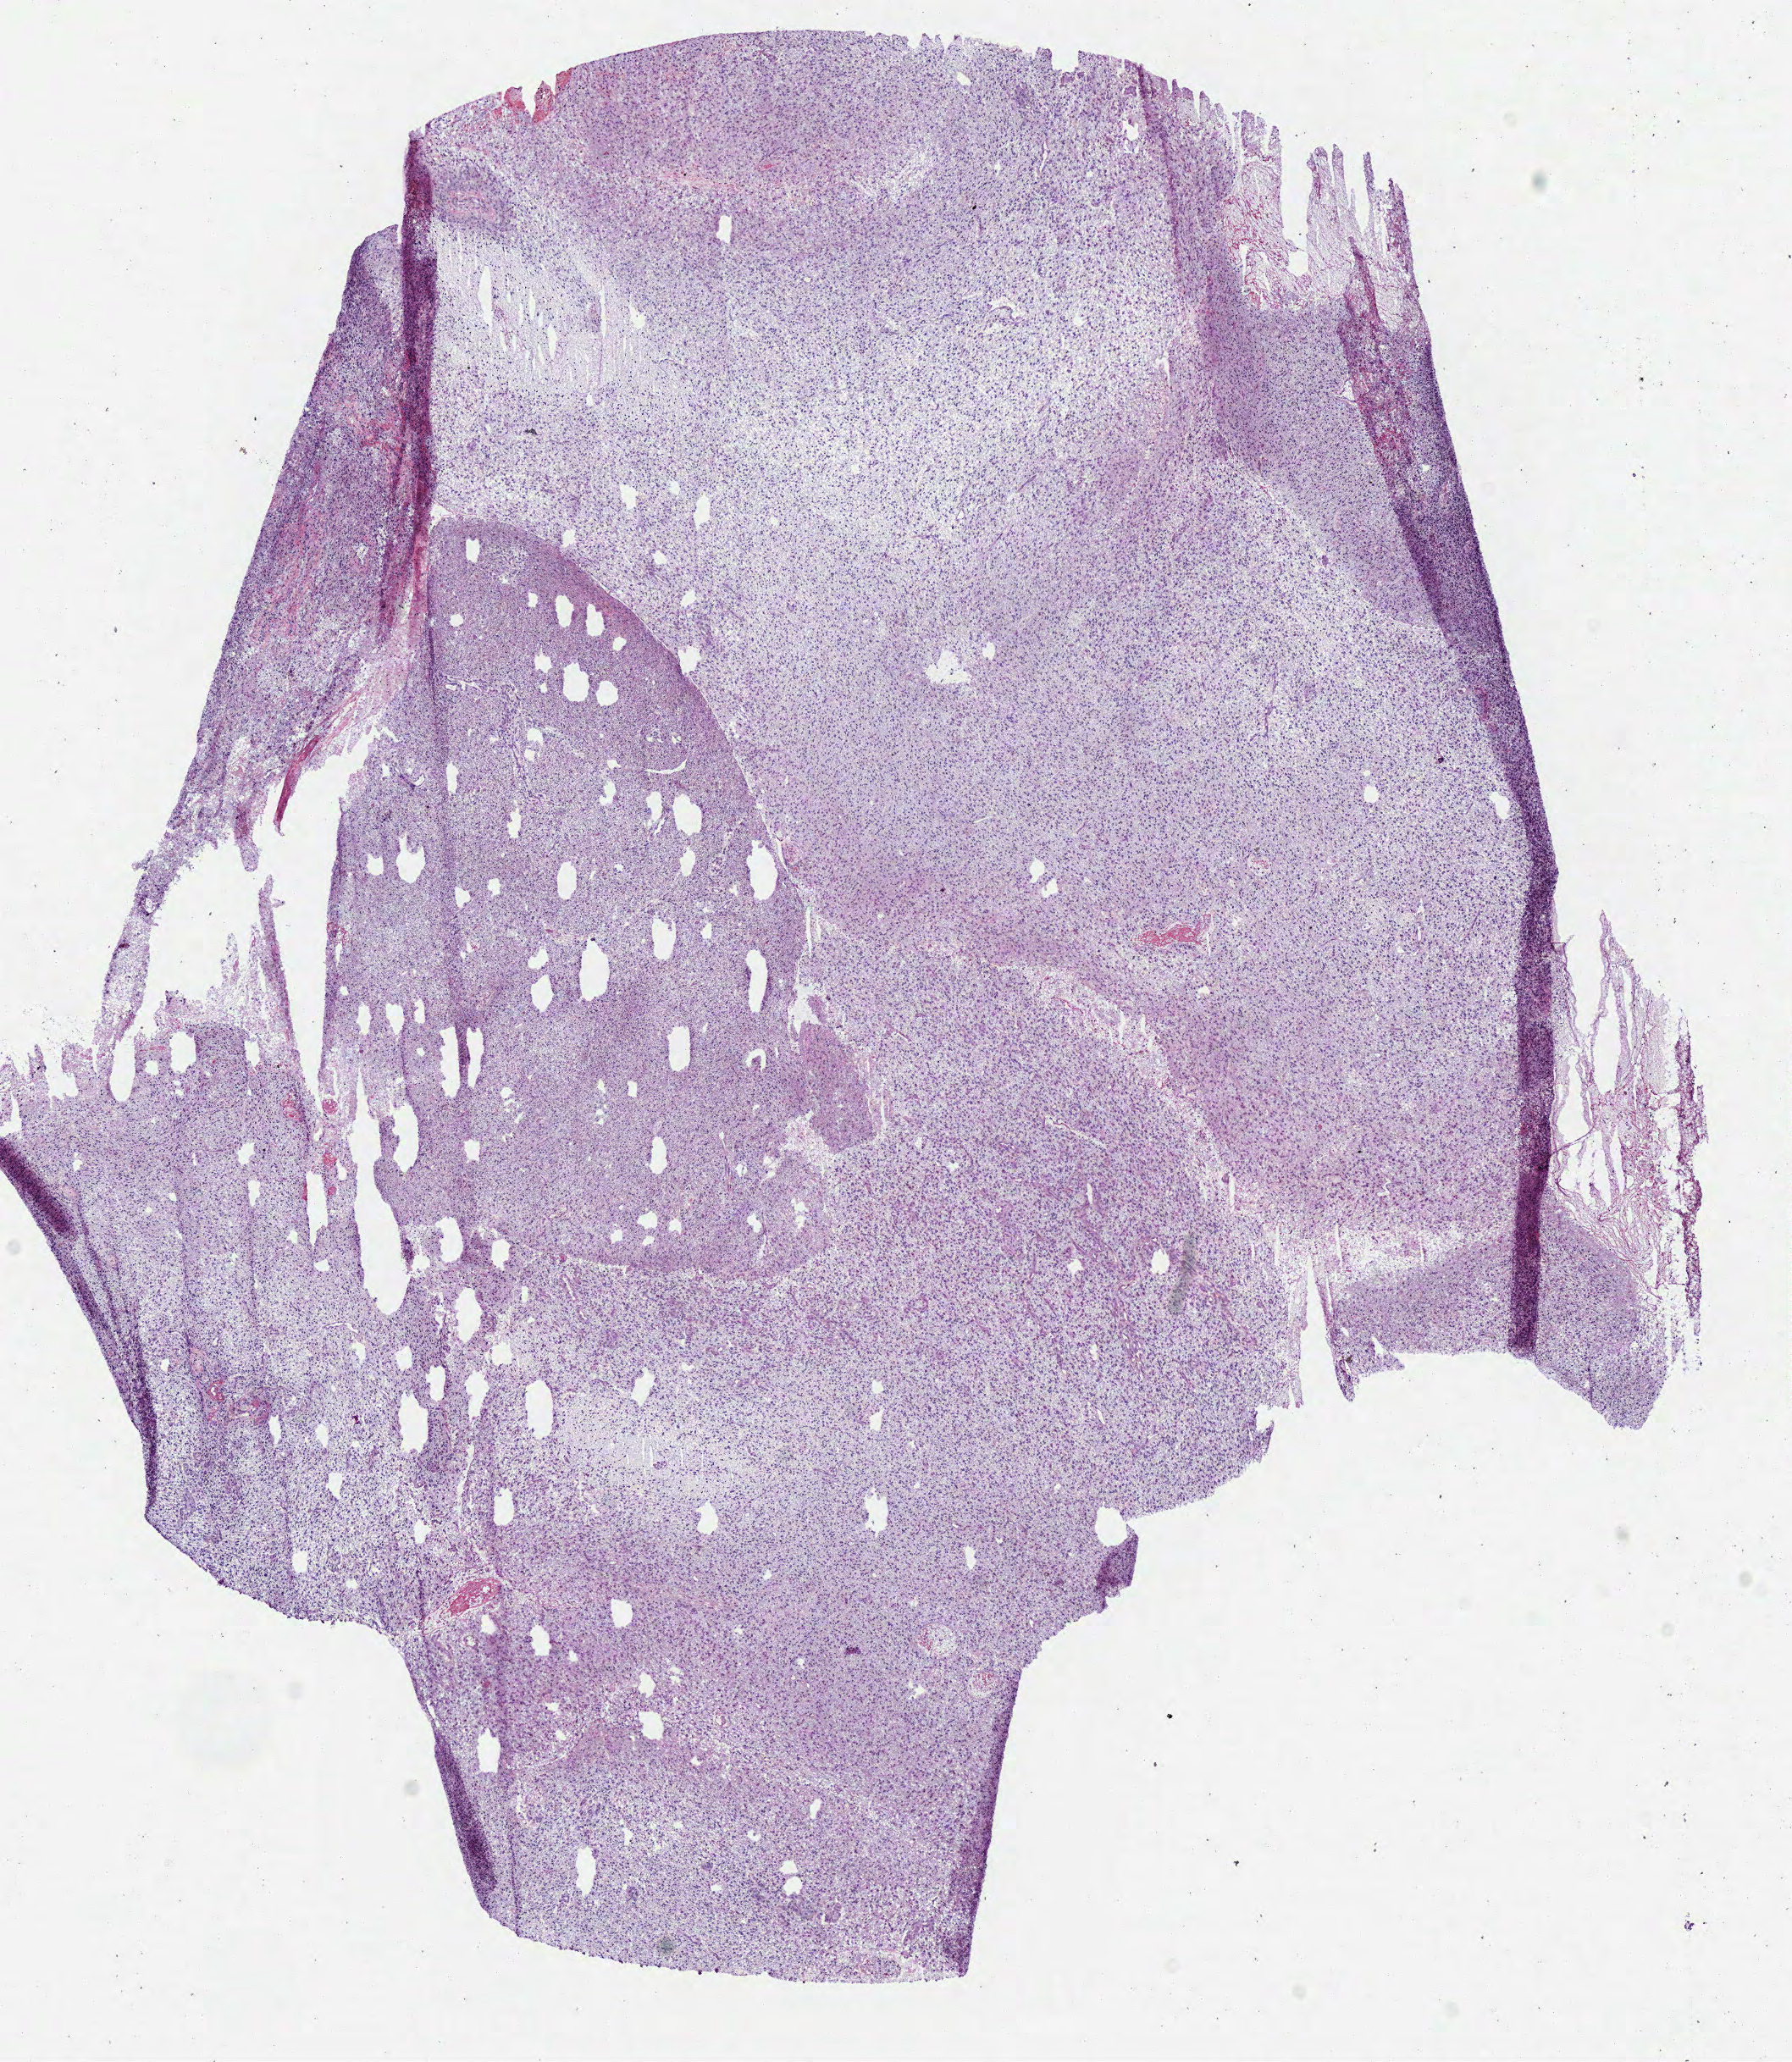
H&E whole-slide image, a low-resolution overview of the entire scanned area, about 8.3 x 9.6 mm. Frozen section from the bottom of the tissue portion. Sample: primary tumour, brain. Patient: male, age at initial diagnosis 64 years. Composition of this section per pathologist review: tumour cells 97%, tumour nuclei 80%, normal cells 0%, stromal cells 0%, necrosis 3%.
Pathologic diagnosis: Glioblastoma.